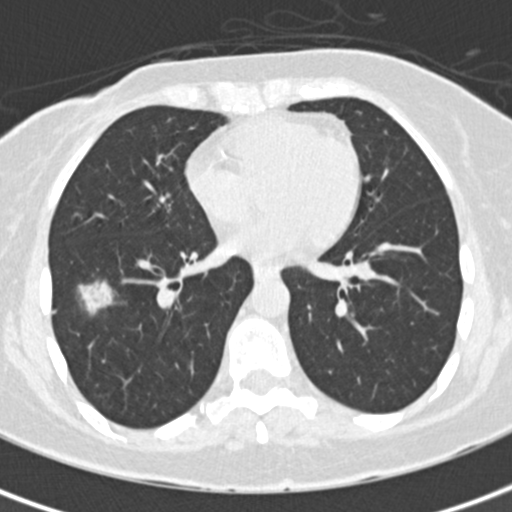
Low-dose screening chest CT, axial slice. First (baseline) screen. Lung window (W 1500 / L -600 HU). Standard (soft-tissue) reconstruction kernel (B30f). Slice 97 of 171 in the series. 512 × 512 image matrix, field of view 284 × 284 mm. Female, age 56 years at enrolment. Former smoker at enrolment.
Expert-annotated lung lesion, bounding box <67,272,129,327> (left, top, right, bottom; pixels). The screening reader recorded 5 non-calcified nodules or masses ≥4 mm on this exam (right lower lobe, right upper lobe, left upper lobe, left lower lobe, left lower lobe); which of them this box marks is not recorded. Later outcome: lung cancer diagnosed 26 days after this screen — bronchiolo-alveolar carcinoma, mucinous, right lower lobe, well differentiated (G1), stage IA (AJCC 6th edition), 19 mm at pathology.